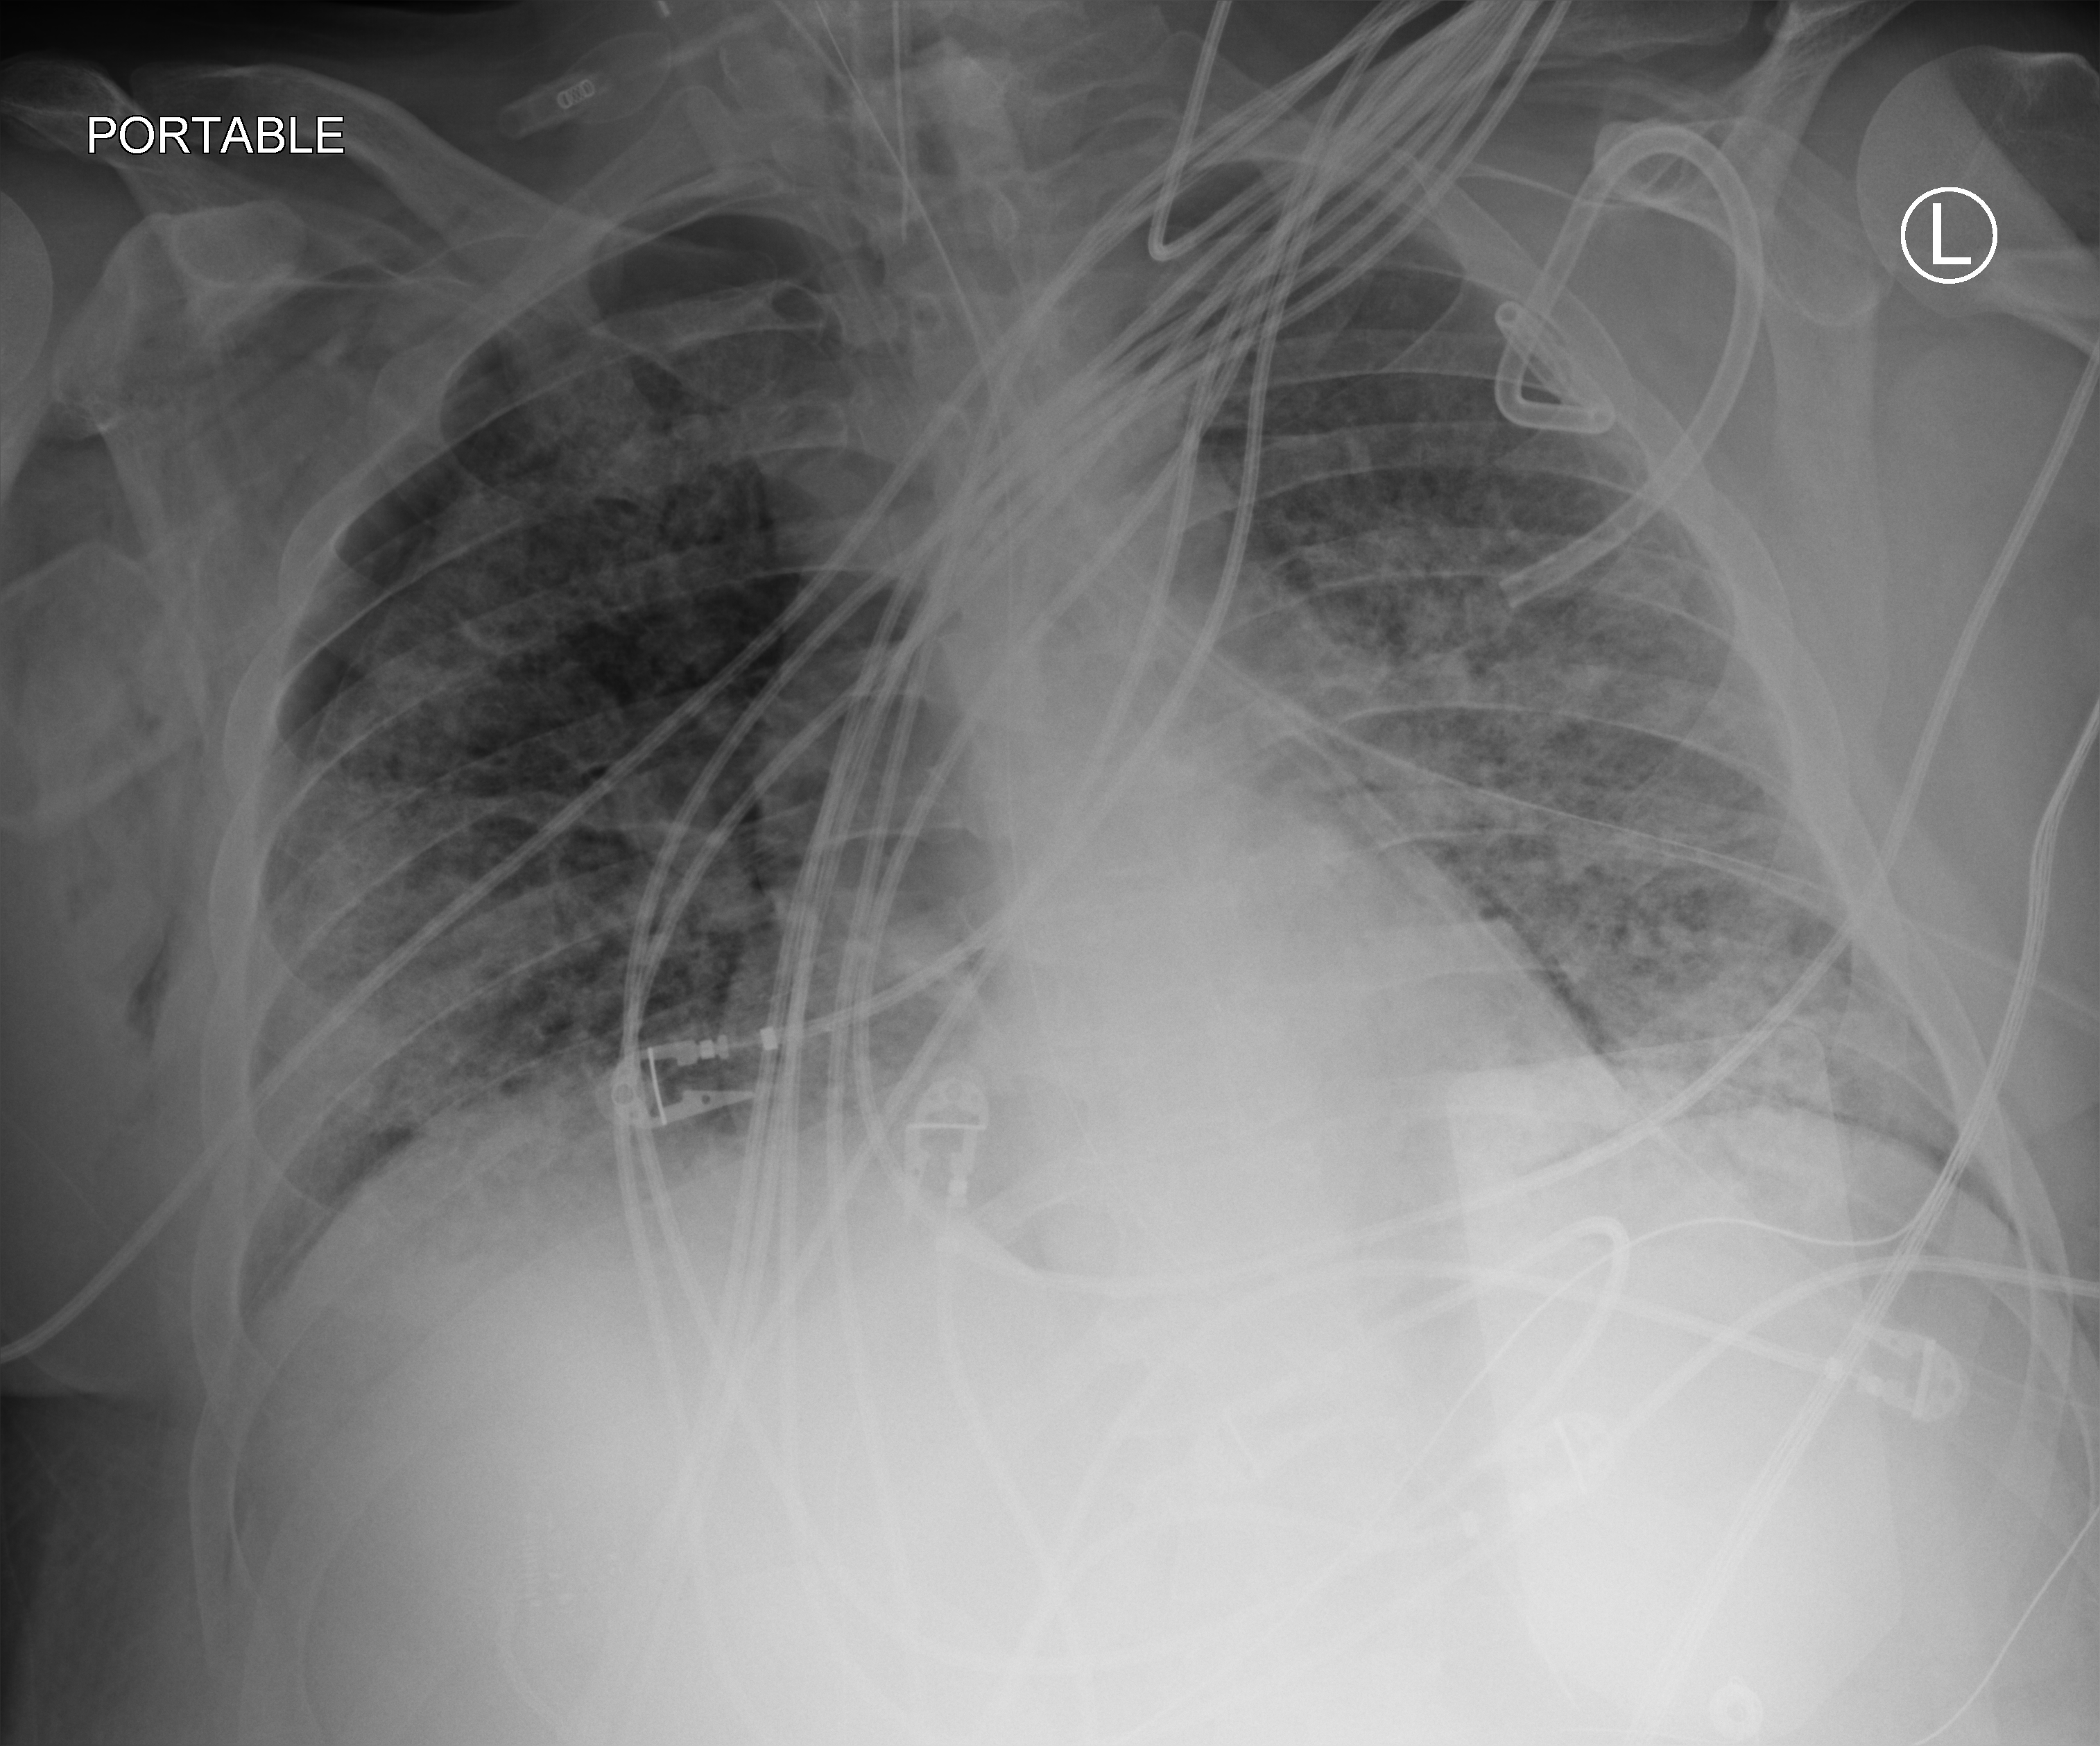
Chest X-ray (portable); anteroposterior (AP) projection. Patient hospitalised with COVID-19, aged 18–59 years.
Admission-level facts for this patient (not findings on this image; timing relative to this image not recorded): length of hospital stay: 31 days; mechanically ventilated during this hospital stay: yes; admitted to intensive care during this hospital stay: yes.